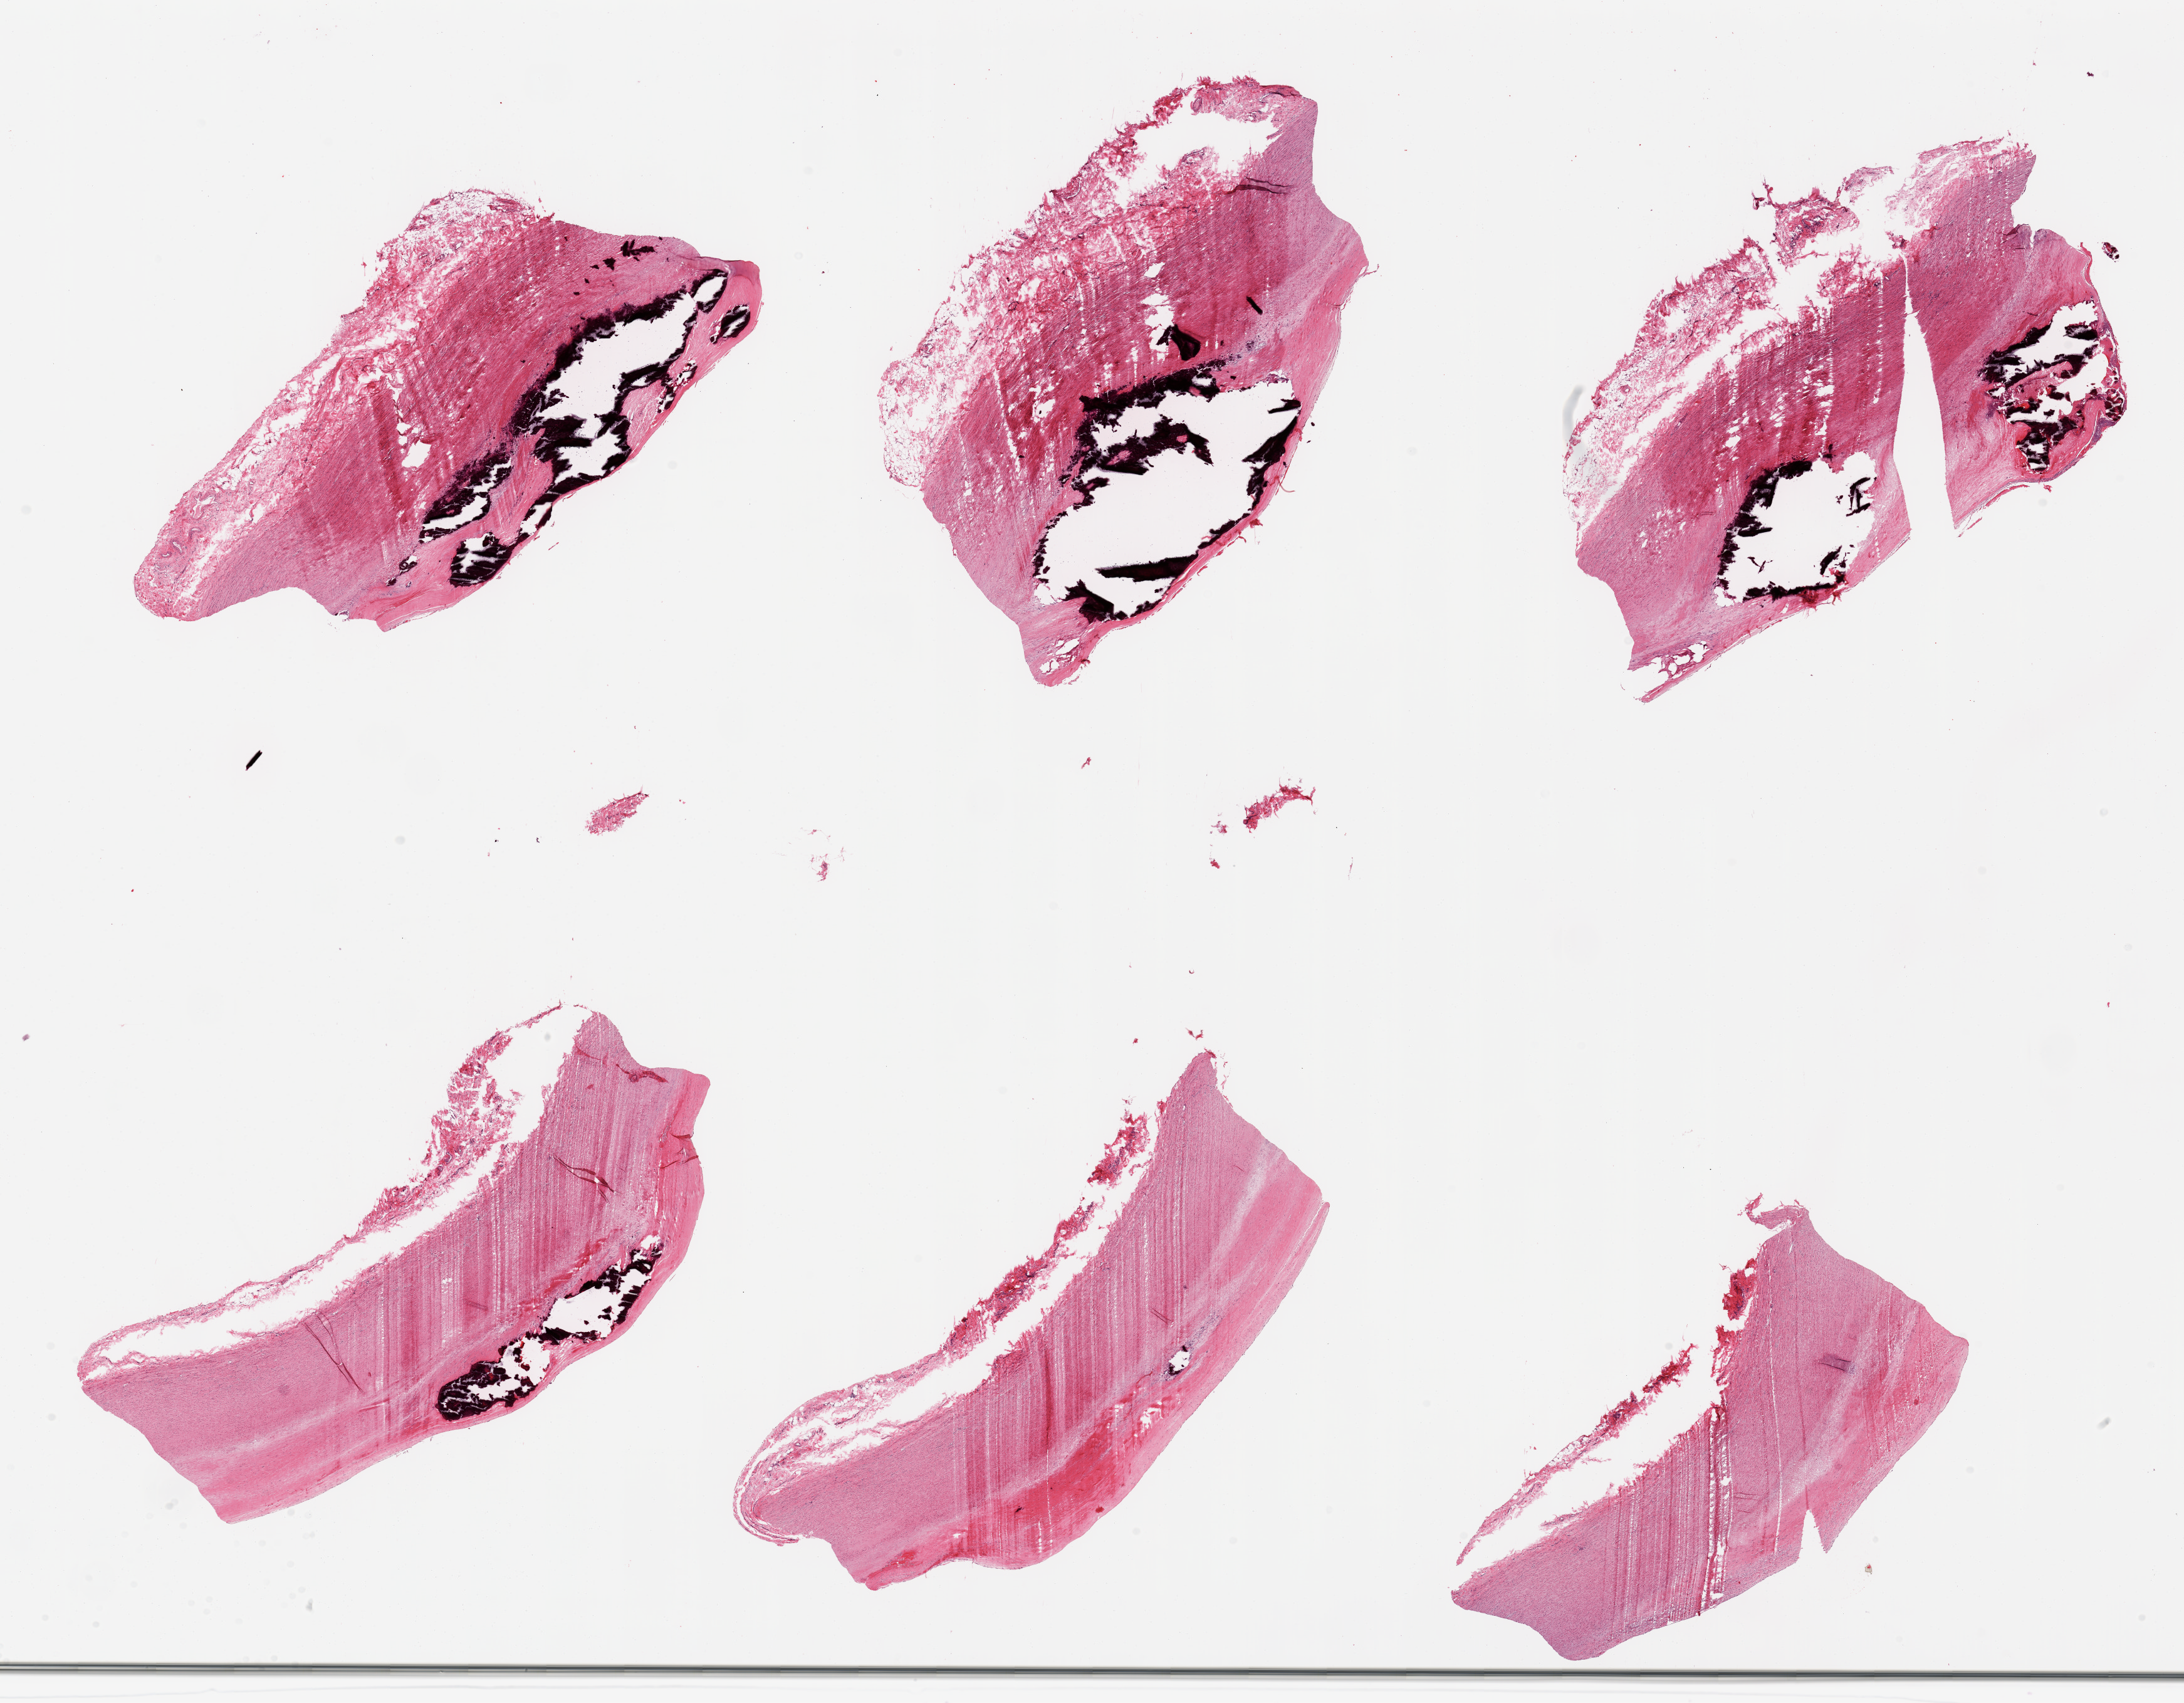
Hematoxylin and eosin (H&E) whole-slide image, a low-resolution overview of the entire scanned area, about 27.6 x 21.5 mm (from a 20x scan). PAXgene-fixed paraffin-embedded (PFPE) section. Sampled site (target tissue): aorta. Tissue donor sample. Donor: male.
* review note (as recorded): 6 pieces: 4 with extensive intimal calcification and atherosclerosis; 2 pieces have thick plaques up to 1.2 mm